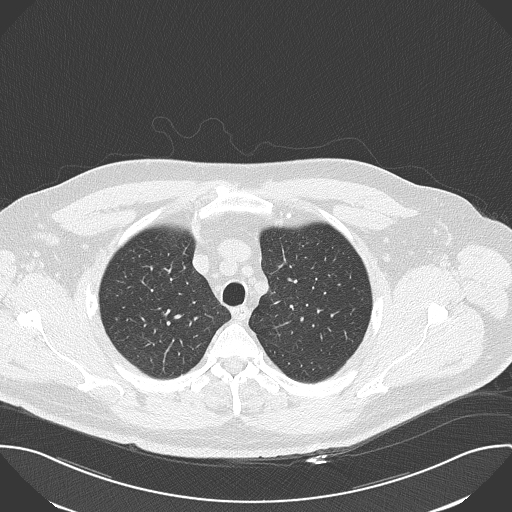
Chest CT (low-dose screening protocol), one axial image, baseline annual screen, lung window (W 1500 / L -600 HU), lung (sharp) reconstruction kernel (B50f), 120 kVp, slice 36 of 156 in the series, 512 × 512 image matrix, field of view 388 × 388 mm. Male participant, aged 56 years at enrolment.
- Expert-annotated lung lesion, bounding box <100,303,134,343> (left, top, right, bottom; pixels).
- Screening reader's record for this exam: no non-calcified nodule ≥4 mm recorded.
- Later outcome: lung cancer diagnosed 476 days after this screen — squamous cell carcinoma, NOS, right upper lobe, moderately differentiated (G2), stage IA (AJCC 6th edition), 10 mm at pathology.